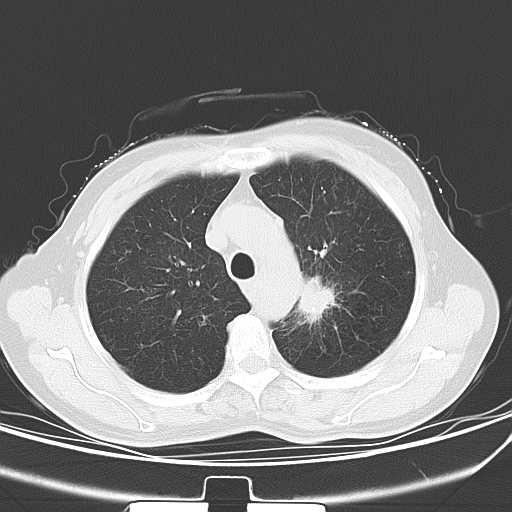
Chest CT, one axial slice; 120 kVp; lung window (W 1500 / L -600 HU); 512 × 512 image matrix. Female patient, age 60 years. From the clinical record (not read from this slice): clinical TNM (as recorded): T1b N0 M0.
Structures marked on this image (bounding box drawn by a radiologist):
- lung tumour (recorded histology: squamous cell carcinoma): box from (x=295, y=267) to (x=337, y=326) px